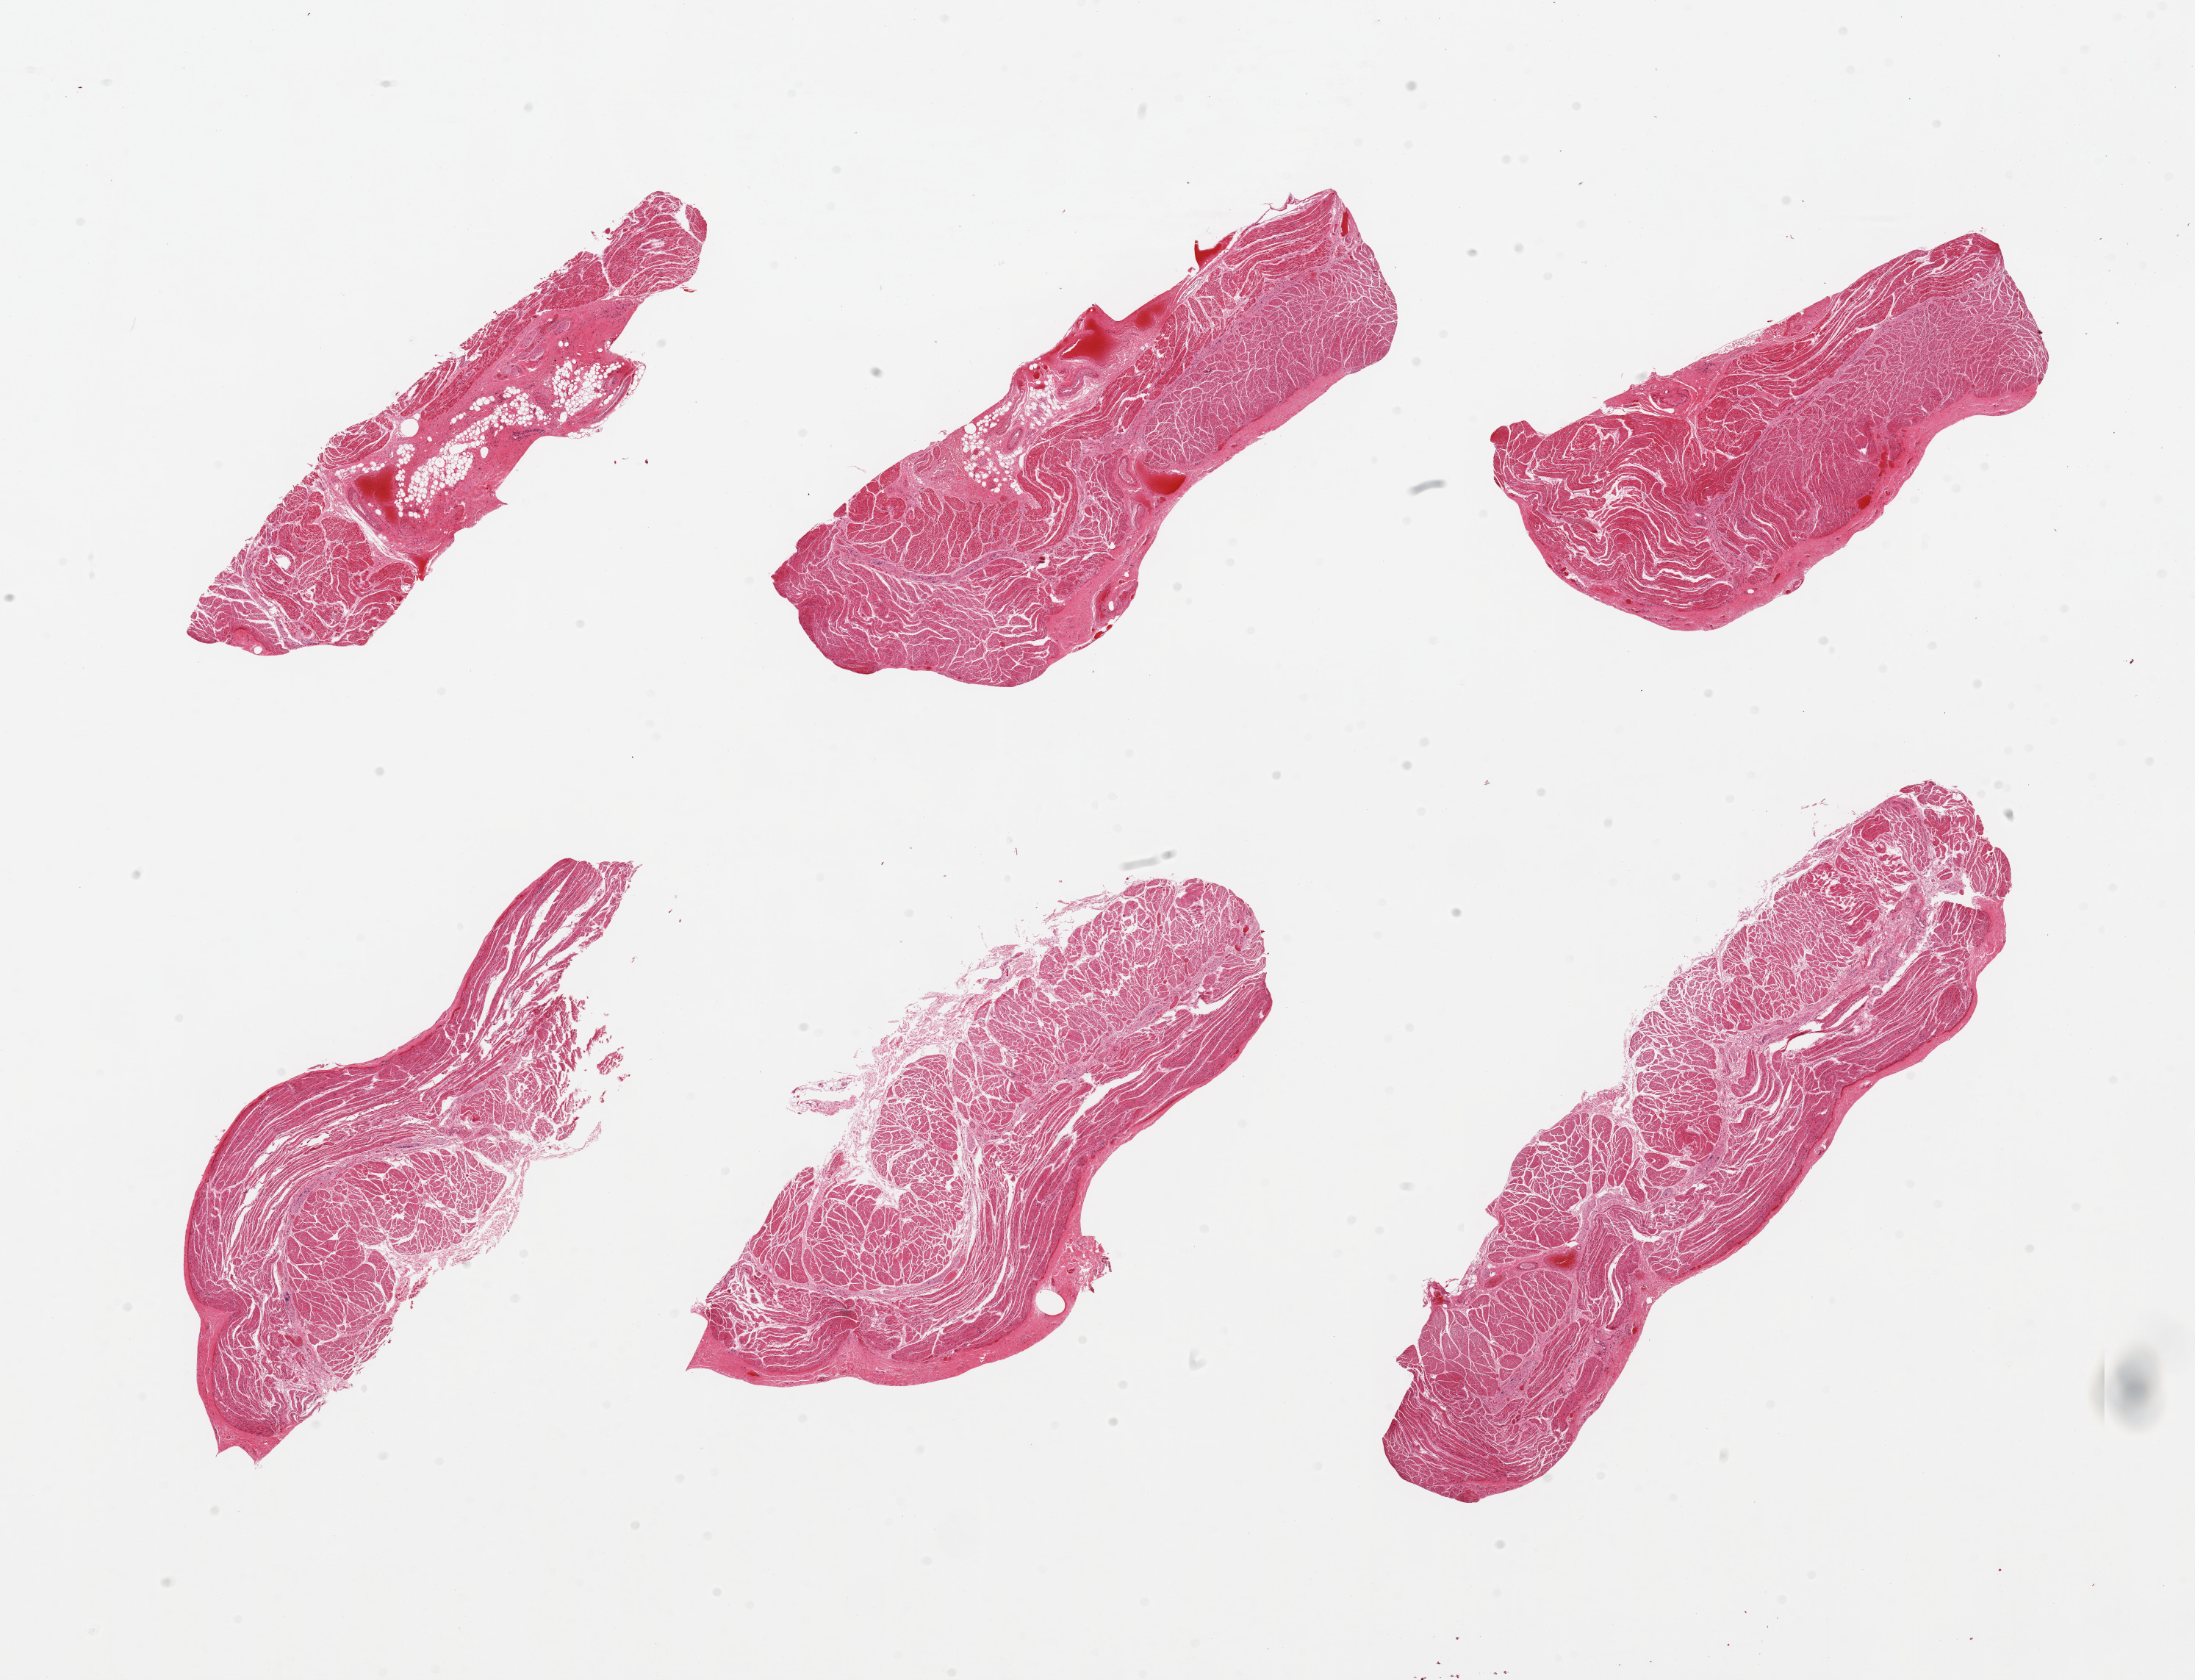
Whole-slide image, haematoxylin and eosin stain, whole scanned area (about 23.6 x 18.1 mm) shown as a low-resolution overview. PAXgene-fixed paraffin-embedded (PFPE) section. Section of esophageal muscle (target tissue). Donor tissue sample. Male donor.
Review note (as recorded): 6 pieces; well trimmed muscle except for 2 pieces with 40% fat.